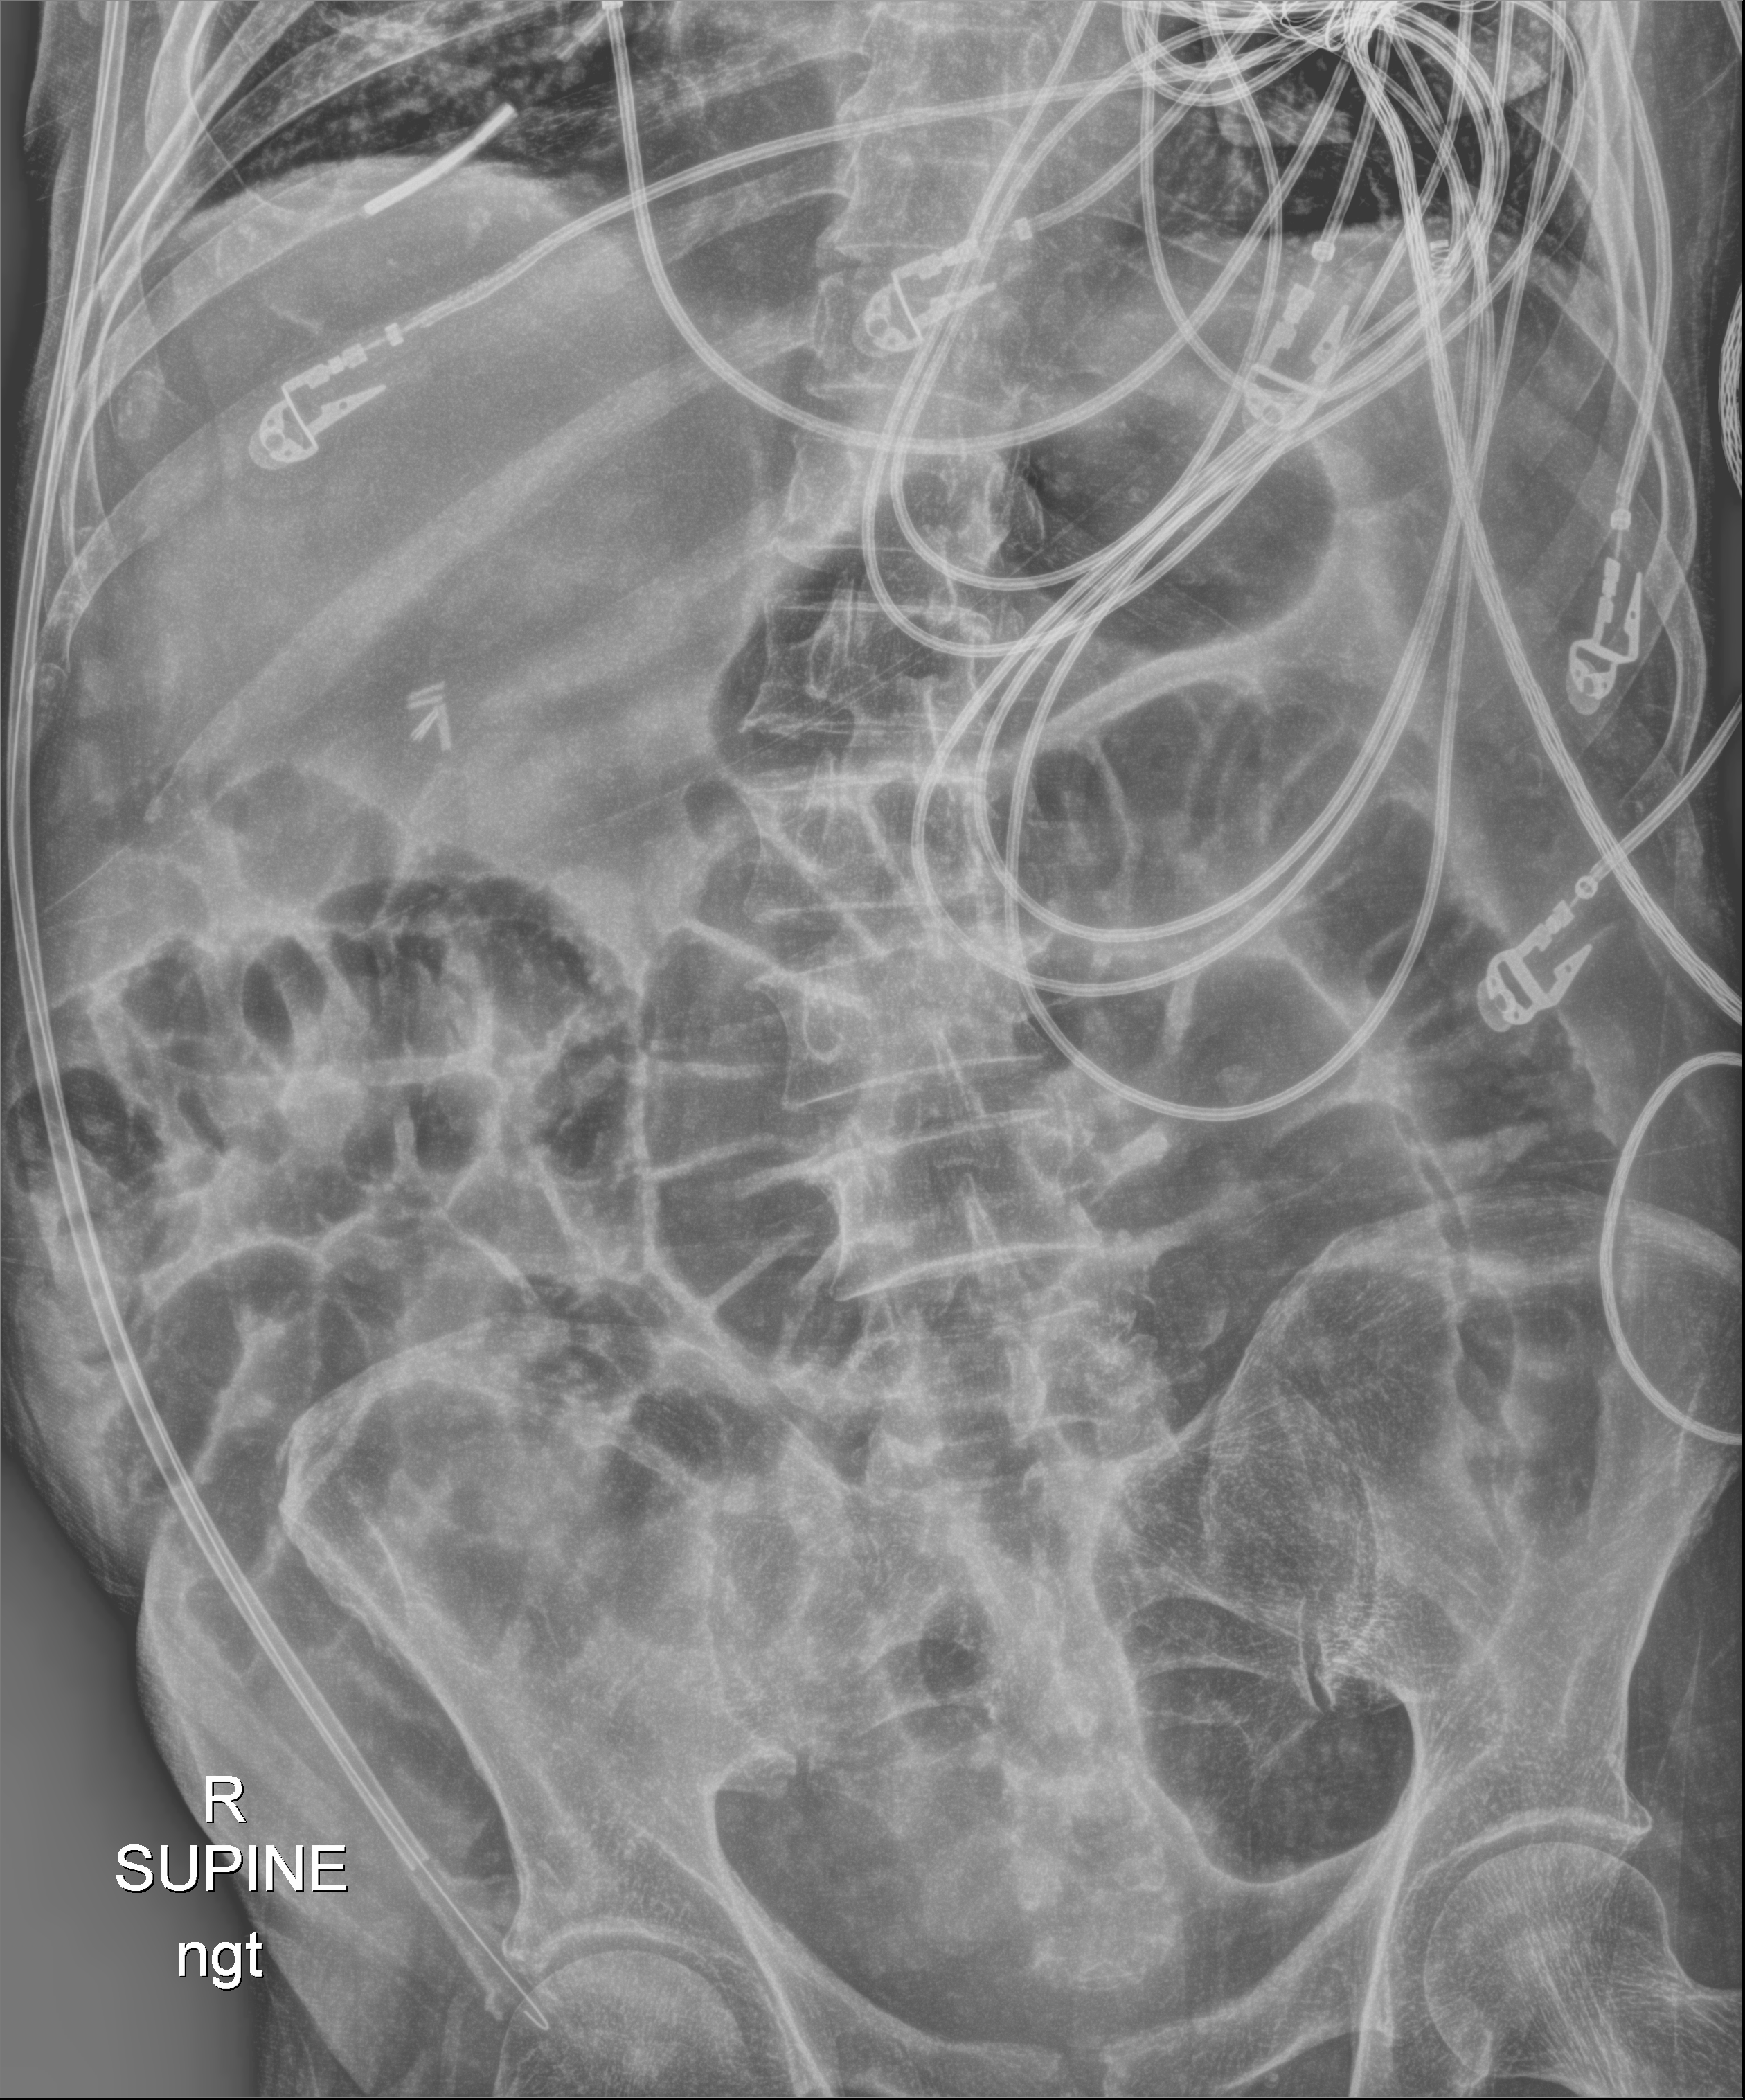
Bedside abdomen radiograph (digital radiography); anteroposterior (AP) projection. Patient hospitalised with COVID-19; male, aged 75–90 years.
Hospital-stay facts (about this admission, not read from this image; timing relative to this image not recorded):
- mechanically ventilated during this hospital stay: yes